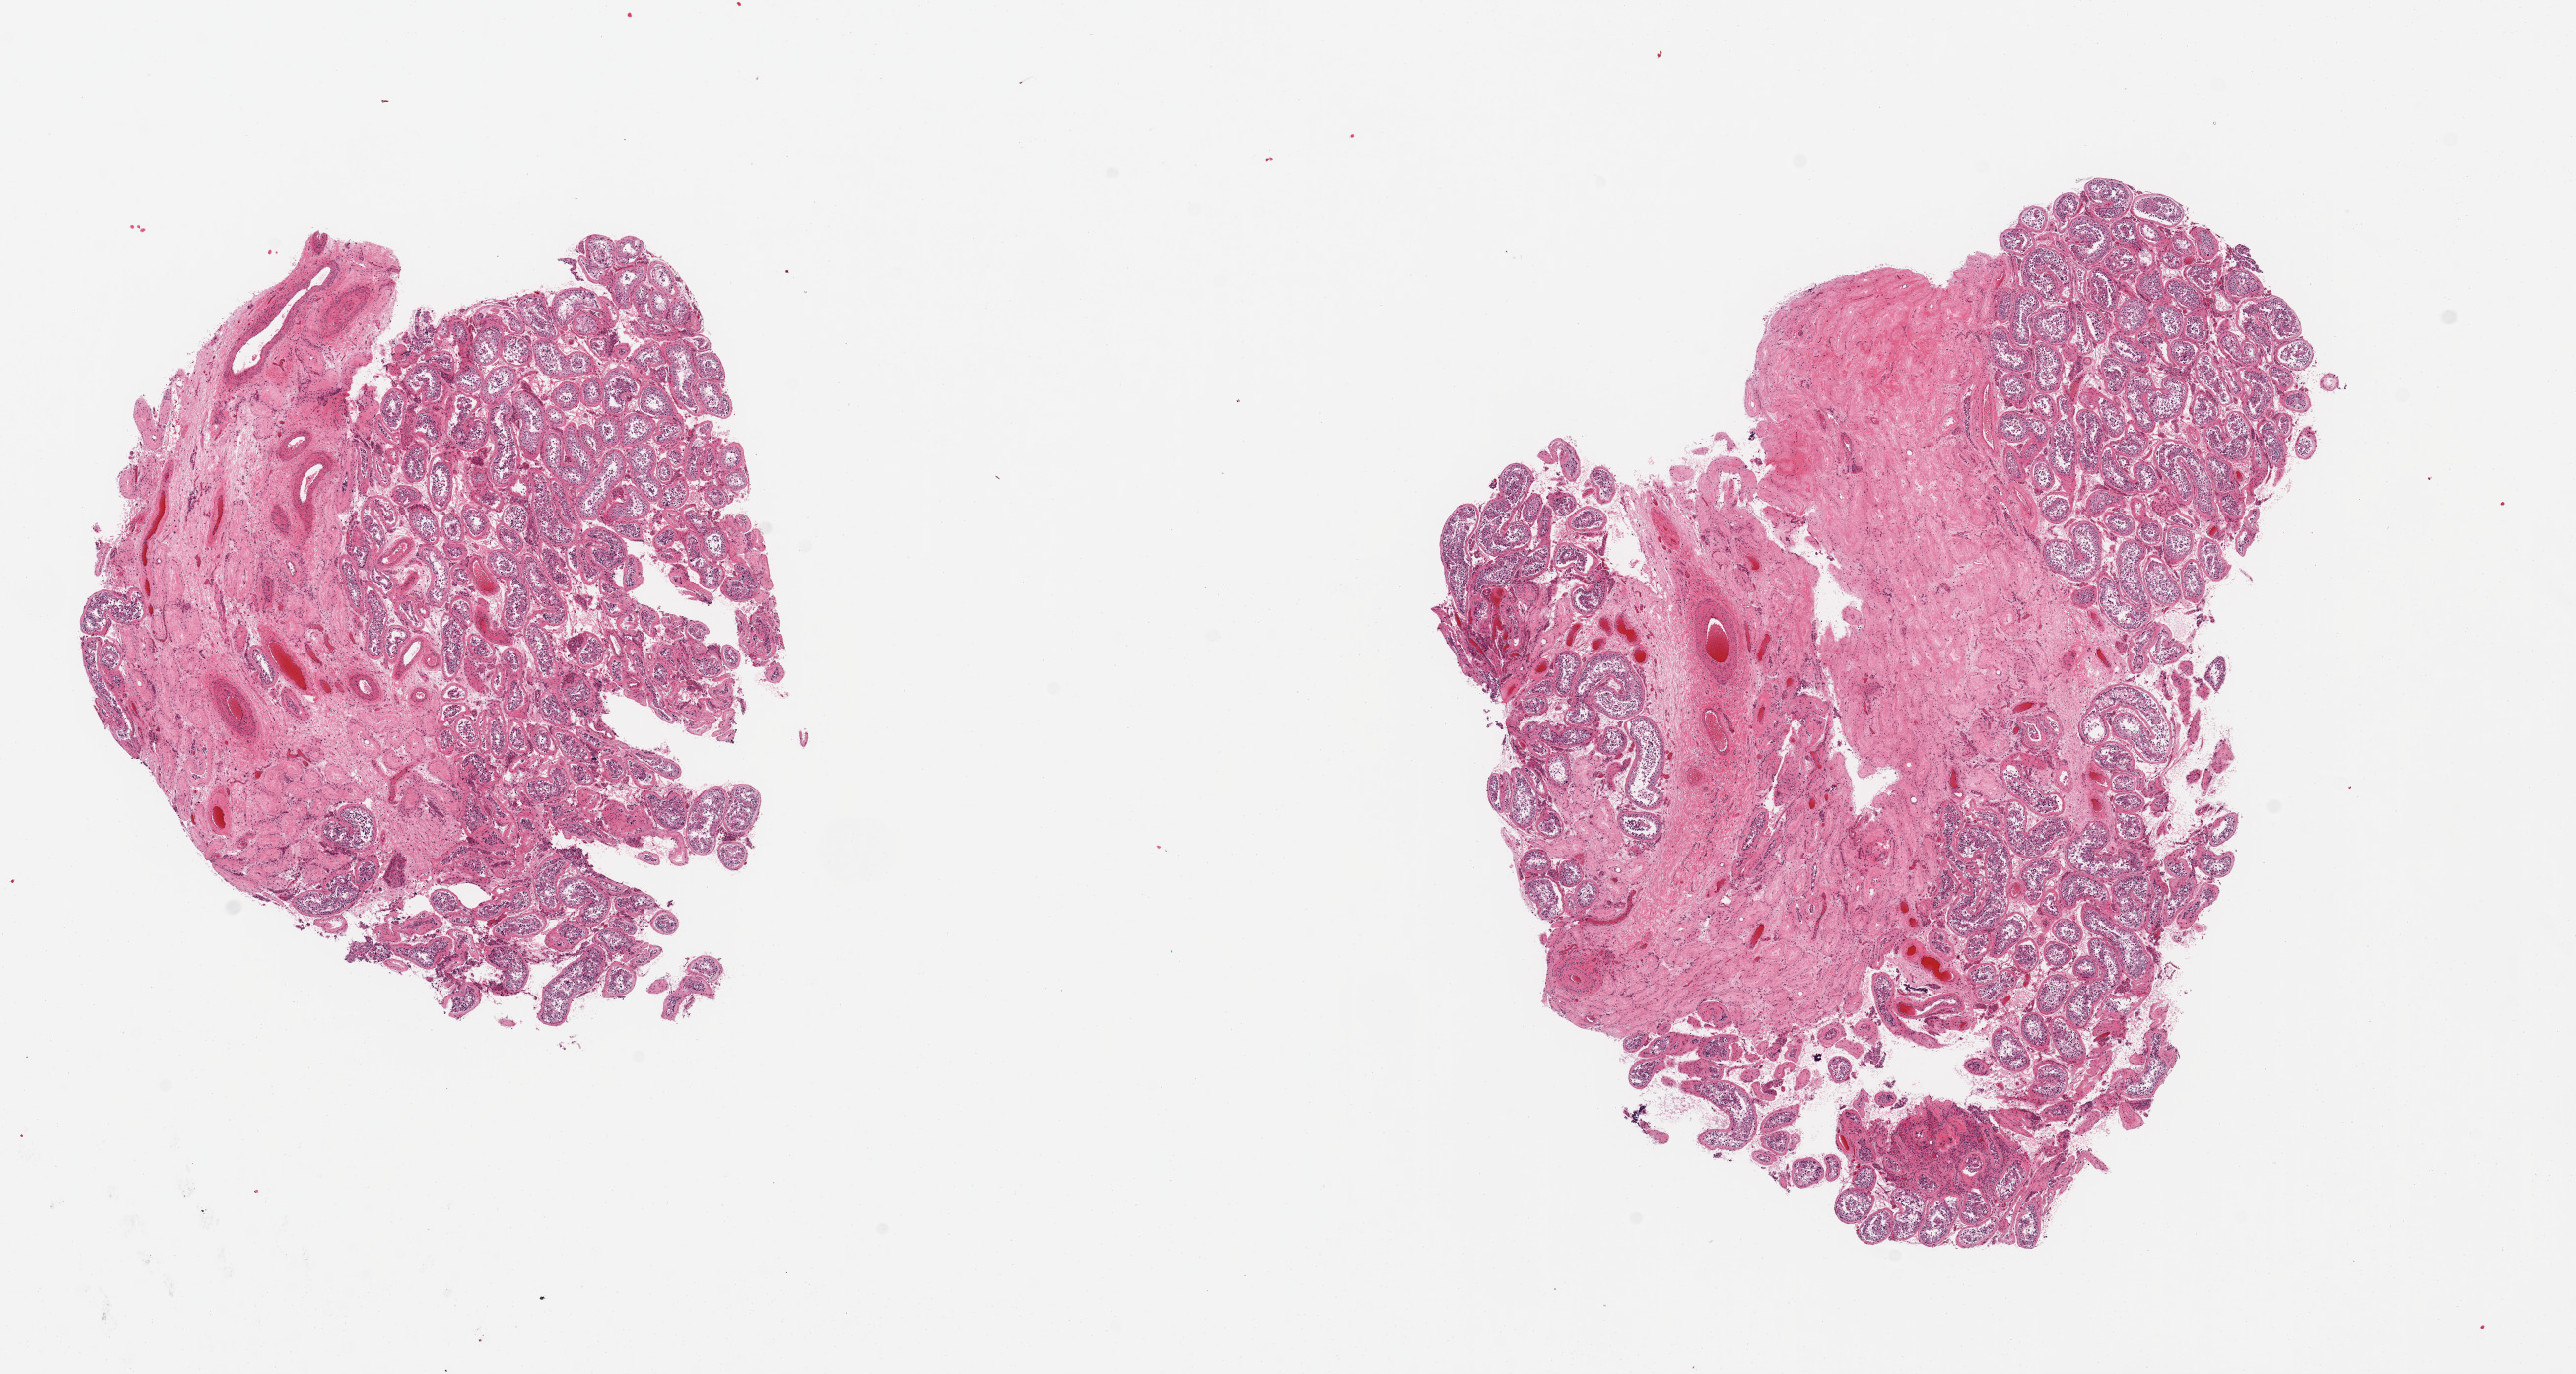
Haematoxylin and eosin whole-slide image — a low-resolution overview of the entire scanned area, about 20.7 x 11.0 mm (from a 20x scan); PAXgene-fixed paraffin-embedded (PFPE) section; target tissue: testis; tissue donor sample. Donor: male.
• review note (as recorded): 2 pieces; spermatogenesis present, some hyalinized tubules